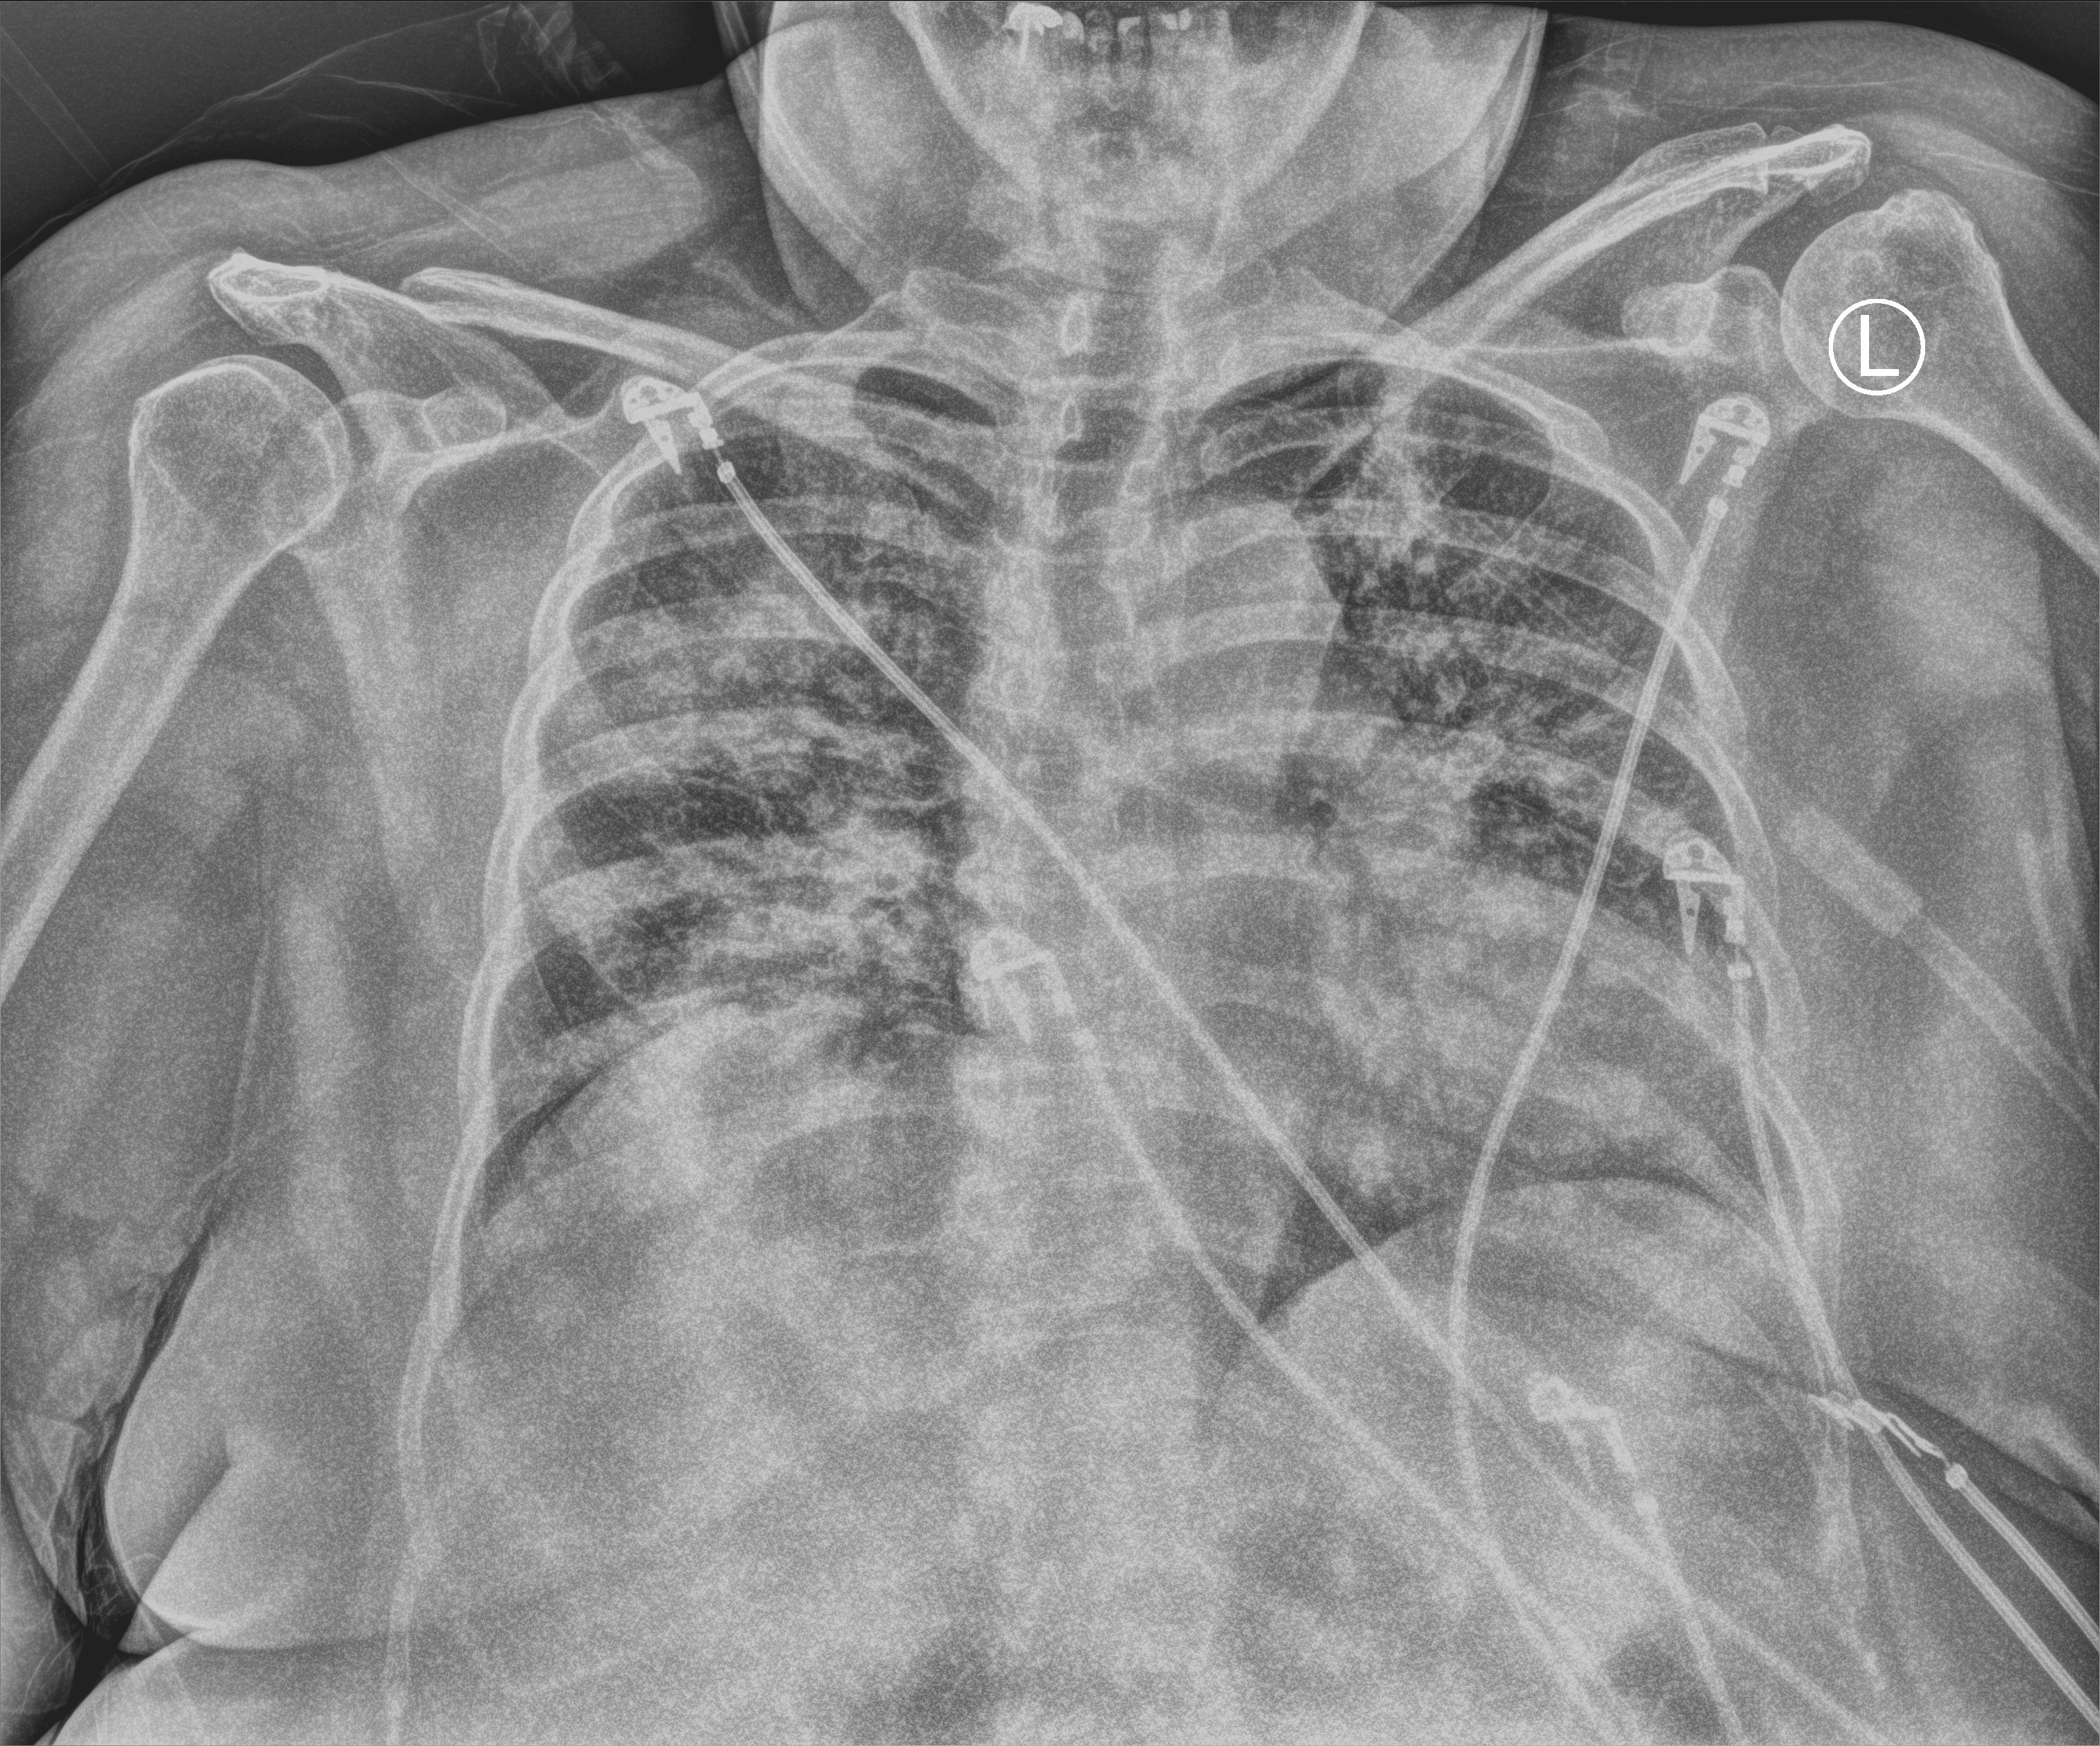
Chest X-ray (portable); anteroposterior (AP) projection. Patient hospitalised with COVID-19; female, aged 60–74 years.
Admission-level facts for this patient (not findings on this image; timing relative to this image not recorded): admitted to intensive care during this hospital stay: yes.